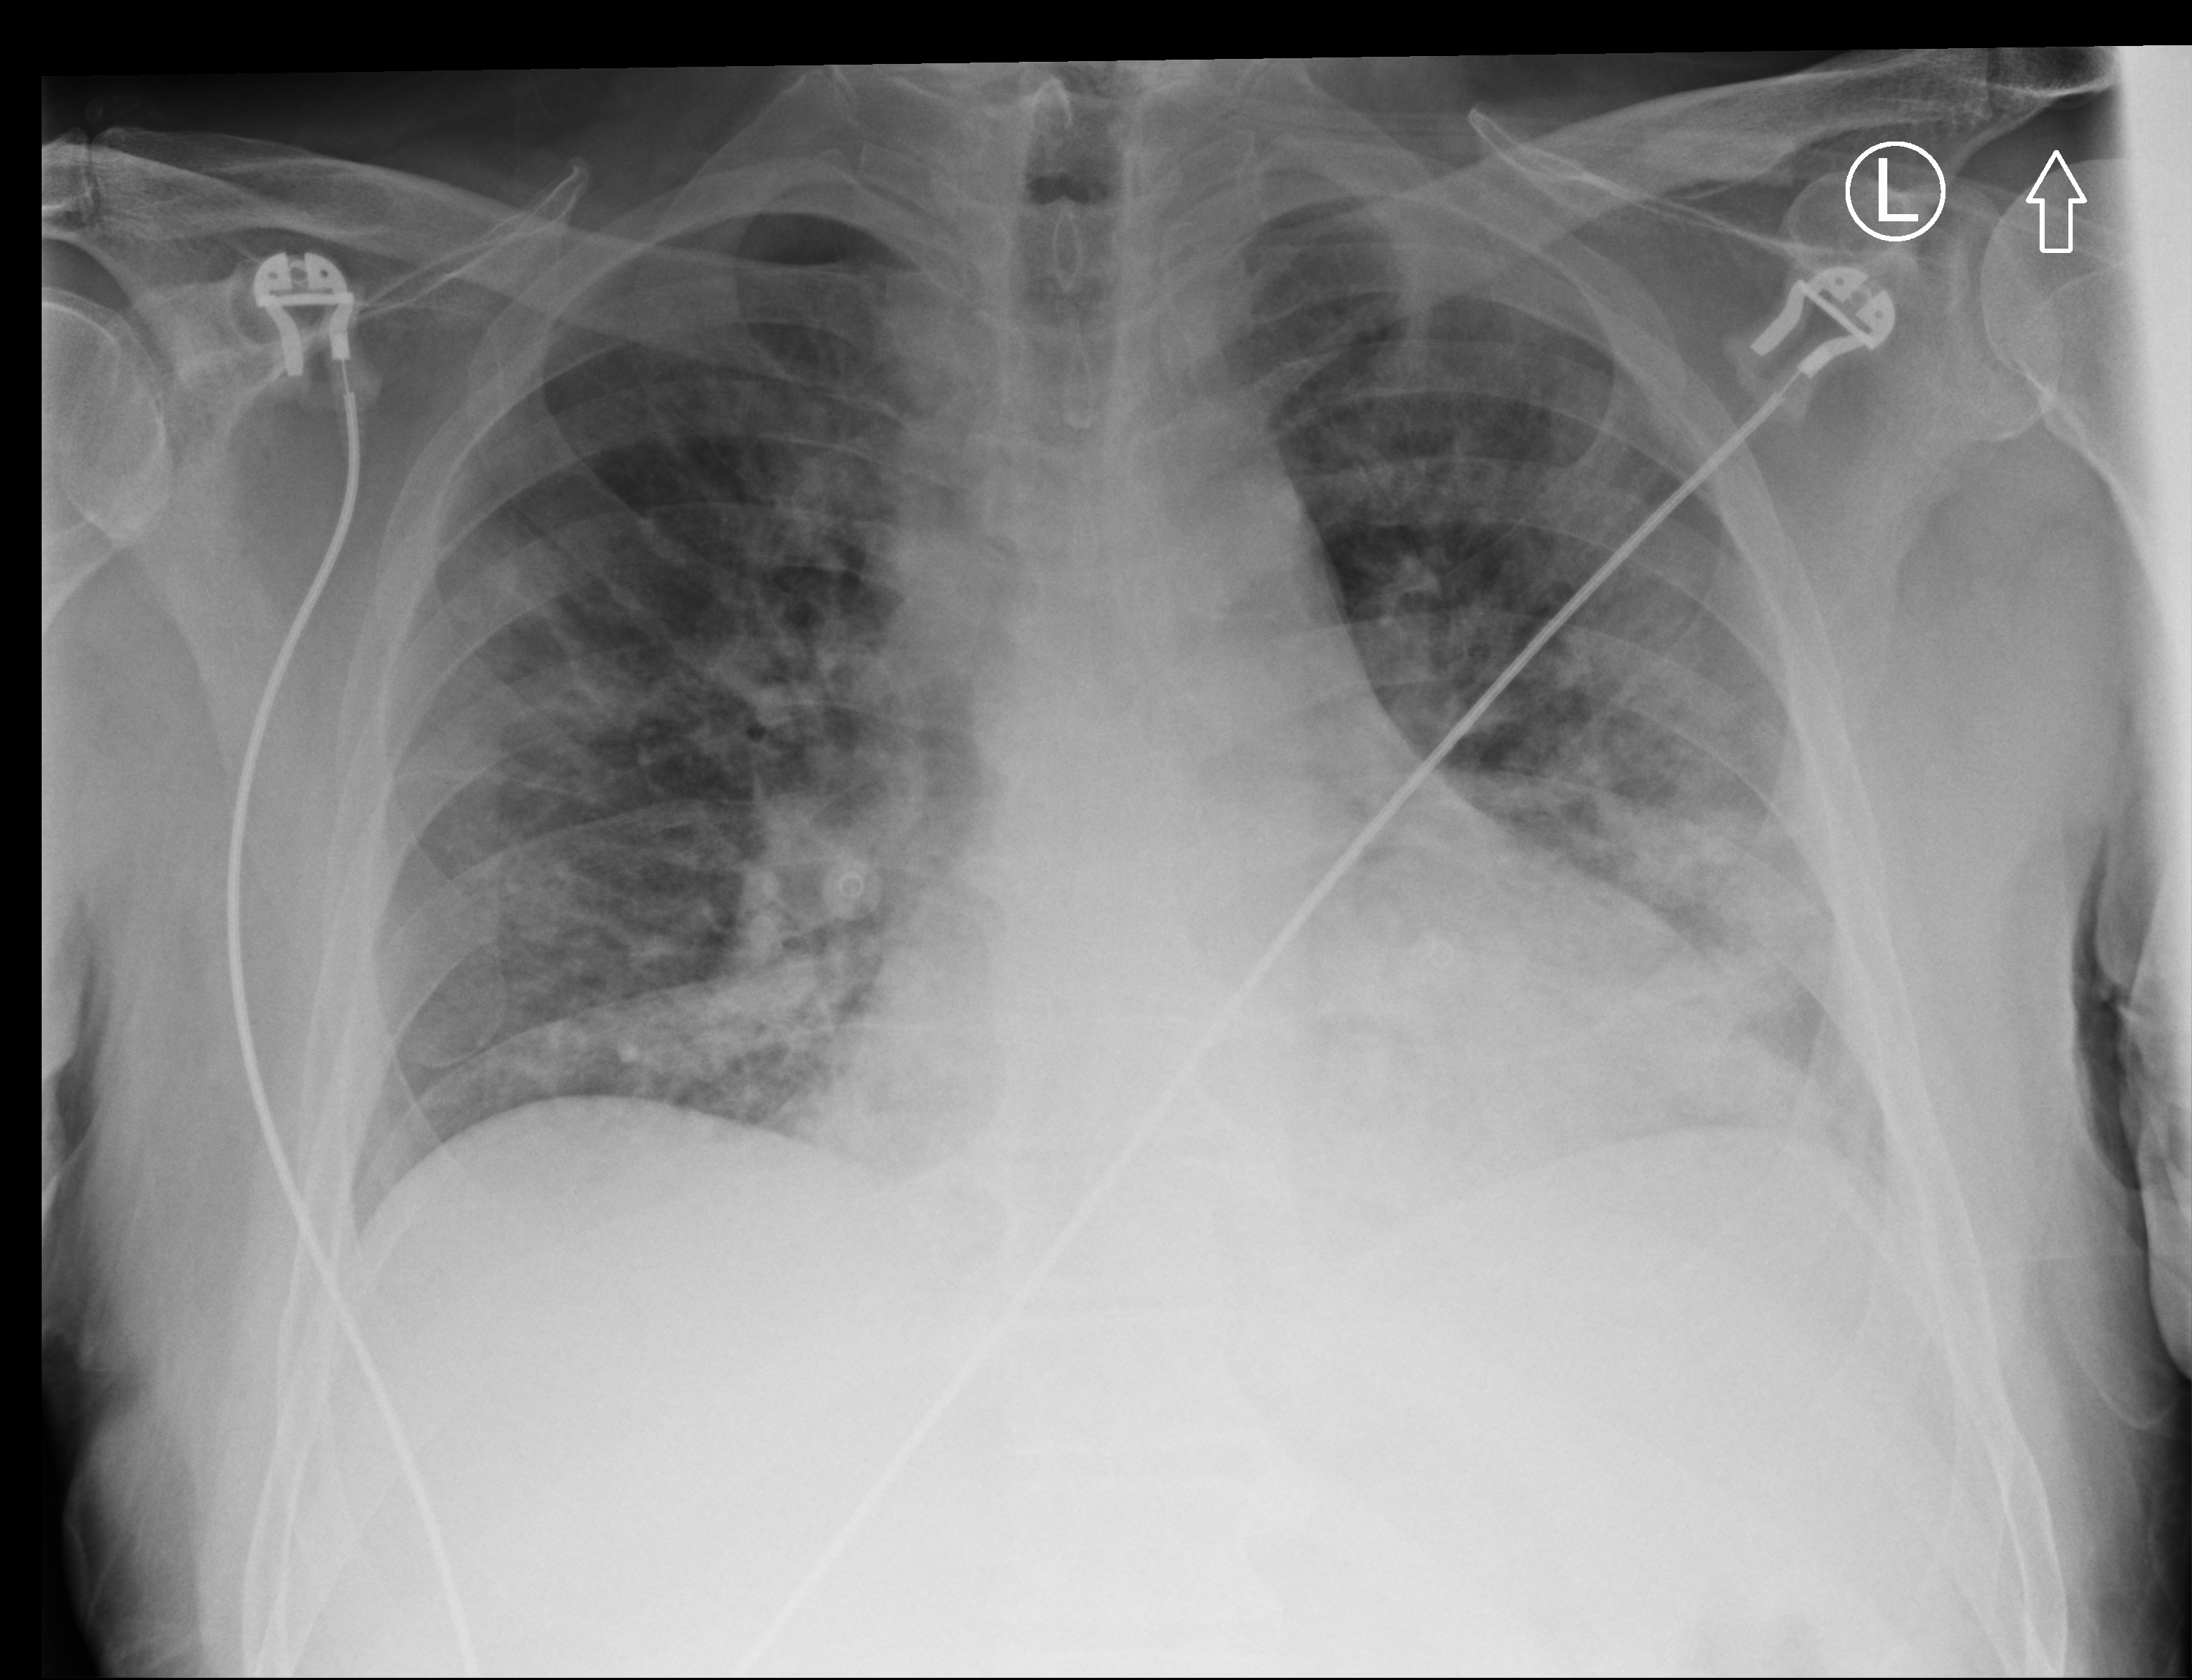
Chest X-ray (portable); anteroposterior (AP) projection. Patient hospitalised with COVID-19; male, aged 60–74 years.
Hospital-stay facts (about this admission, not read from this image; timing relative to this image not recorded): COPD (admission record): no; admitted to intensive care during this hospital stay: yes.